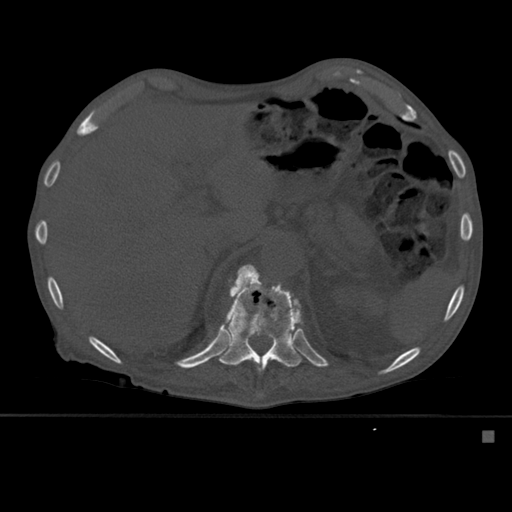
CT including the spine, one axial slice; slice 279 of 527 in the series (ordered by position); bone window (W 1800 / L 400 HU); 1.5 mm slice thickness; 512 × 512 image matrix, field of view 373 × 373 mm. Patient: male, 78 years. Case-level facts recorded for this patient, not image findings: primary cancer: prostate.
Outlined on this slice (semi-automatic segmentation, software-assisted and operator-edited):
- T11 vertebra: bounding box [x1, y1, x2, y2] px = [220, 264, 292, 367]
- T12 vertebra: [219, 266, 303, 396]
- T9 vertebra: [225, 344, 231, 360]